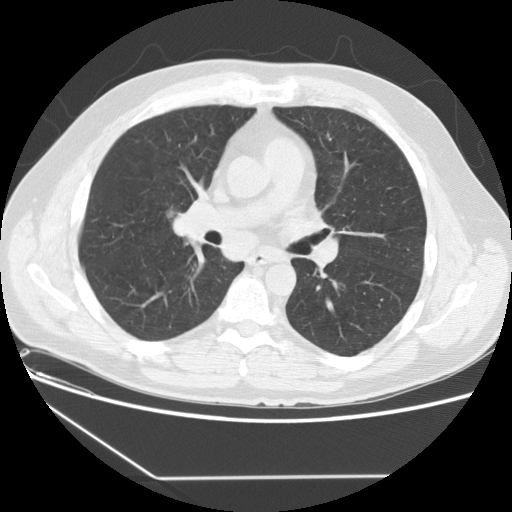
Low-dose screening chest CT, one axial slice. Slice 83 of 154 in the series (ordered by position). Reconstruction kernel STANDARD. Lung window (W 1500 / L -600 HU). 2.5 mm slice thickness. 512 × 512 image matrix, field of view 370 × 370 mm.
Structures marked on this image (outlined manually by an expert reader):
- lesion 1 (tumor, middle lobe of right lung): bounding box (x1, y1, x2, y2) in pixels: (171, 215, 202, 239)